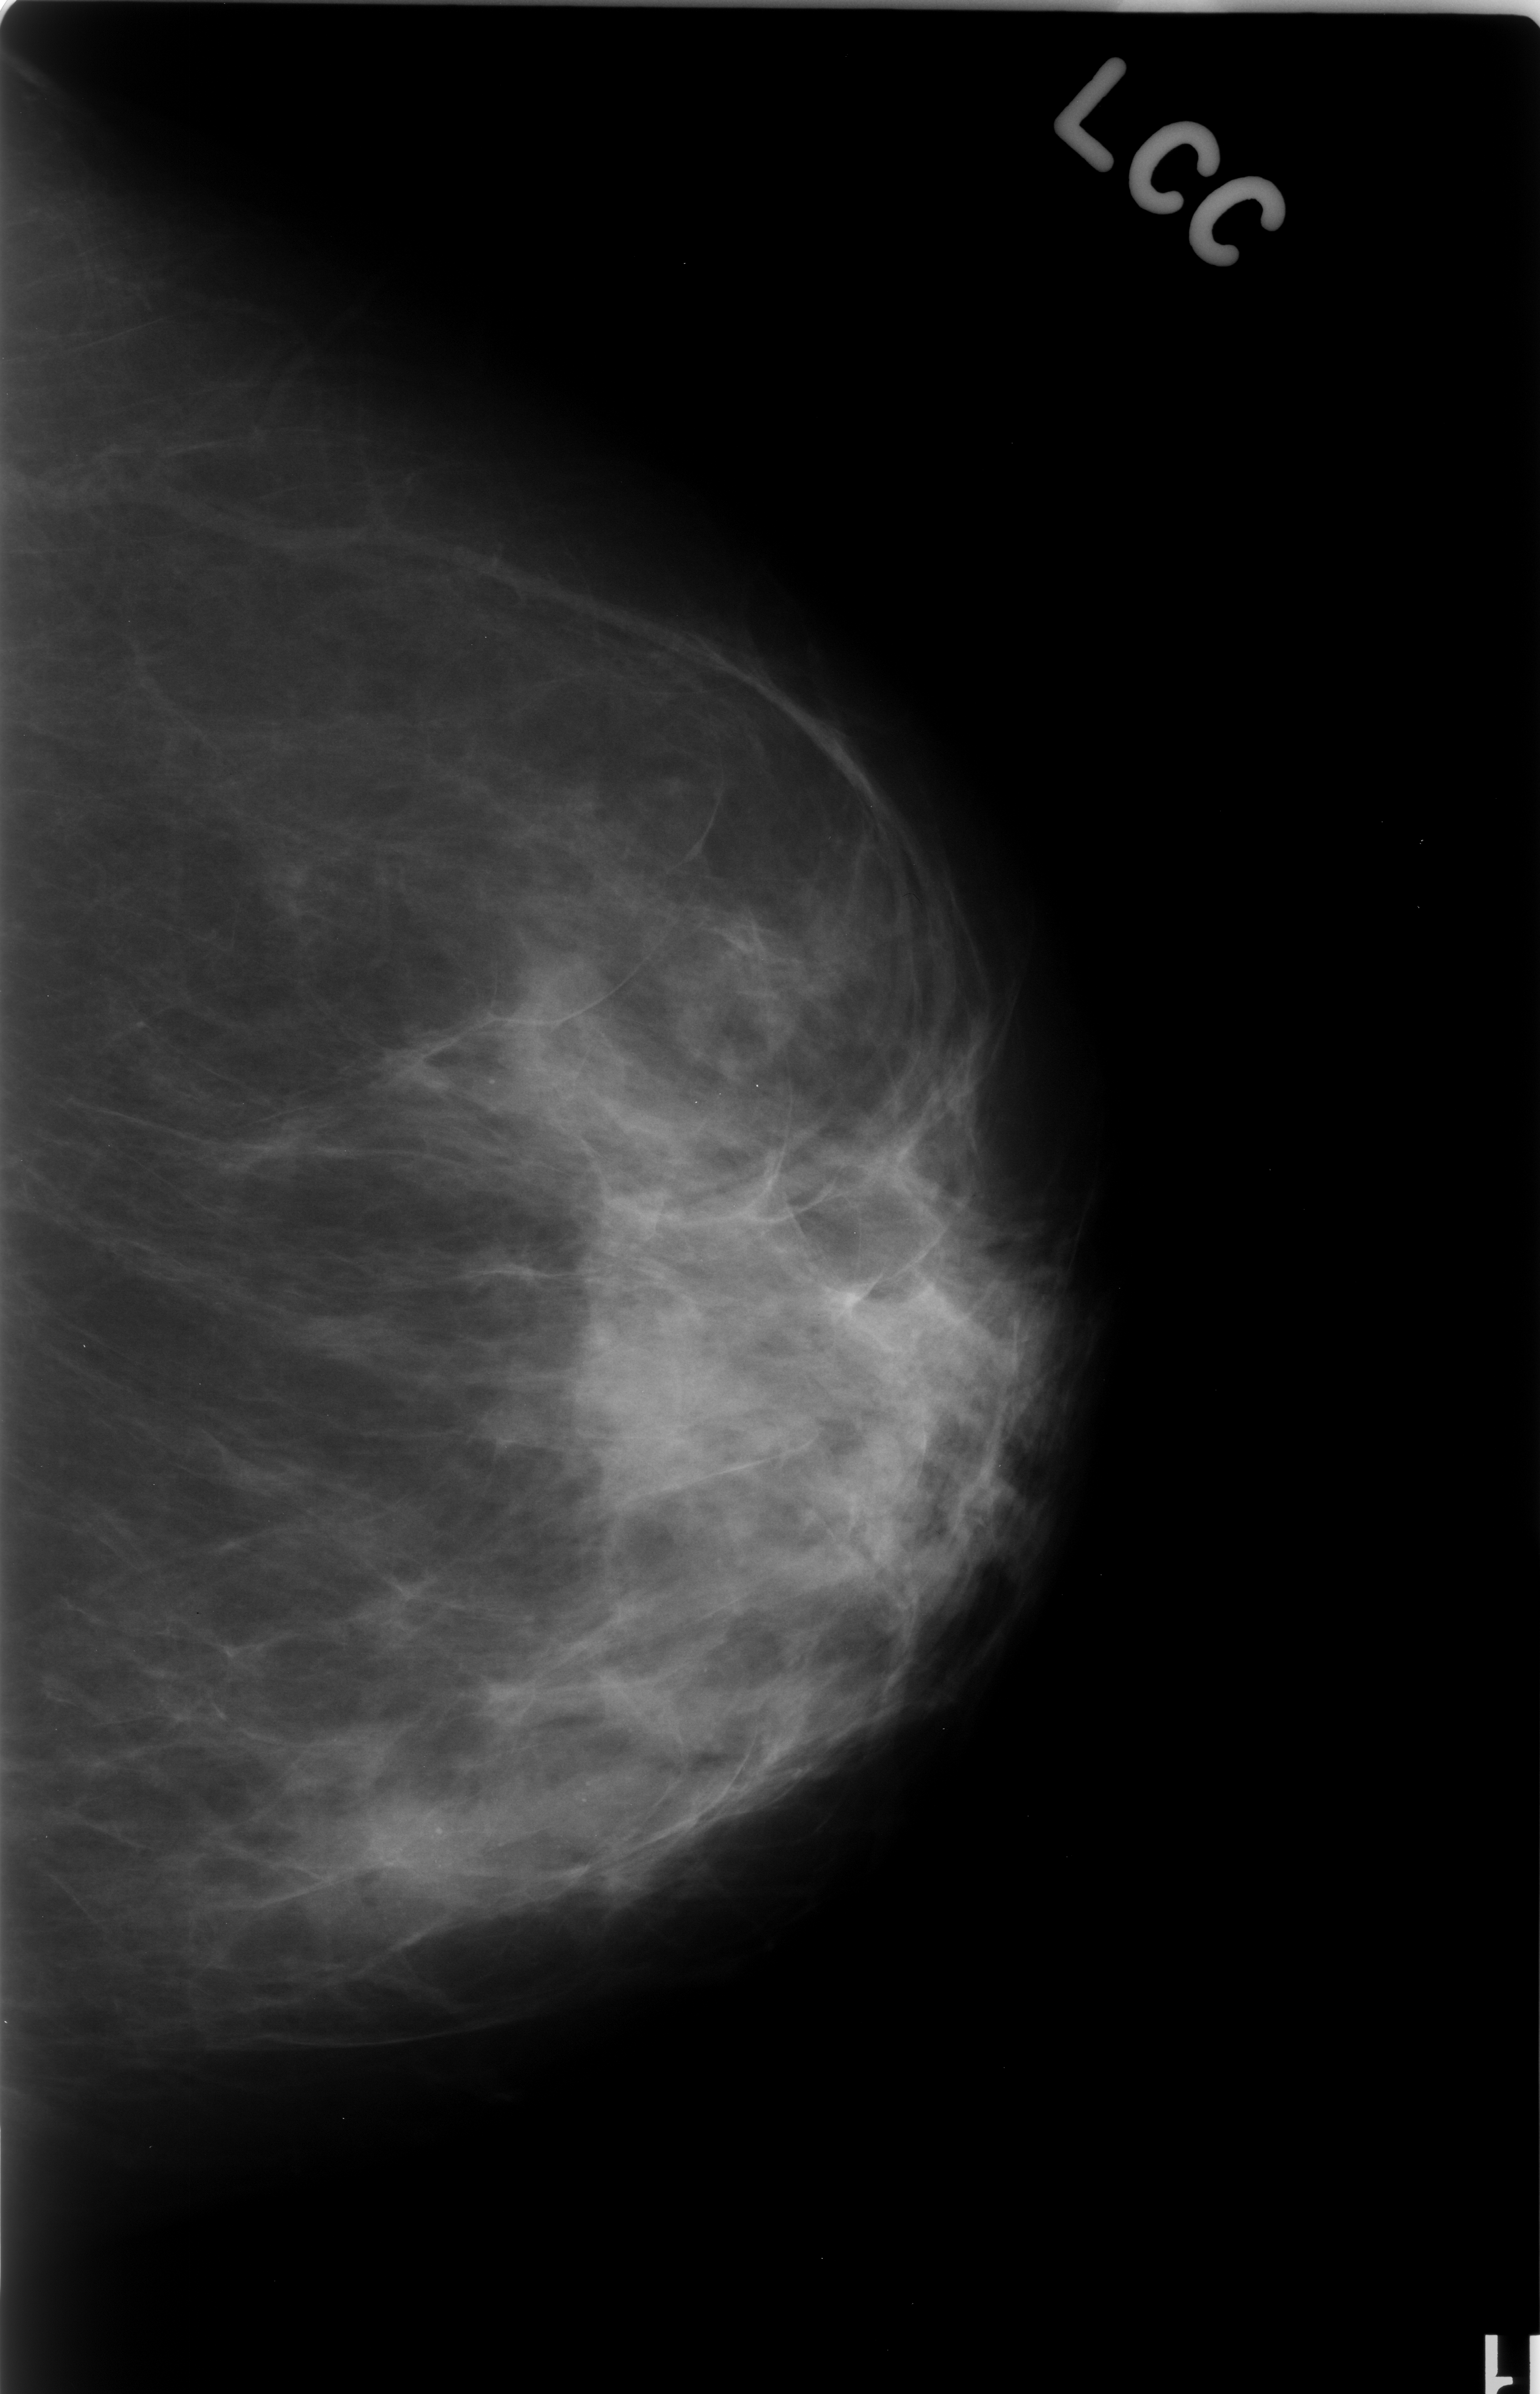
Digitized screen-film mammogram; left breast; CC view; breast composition: scattered fibroglandular densities (BI-RADS density category 2 of 4).
Marked abnormality: calcifications, morphology amorphous, distribution segmental; BI-RADS assessment category 4; subtlety rating 2 on a 1 (subtle) to 5 (obvious) scale; pathology result (as recorded, not read from the image): benign.